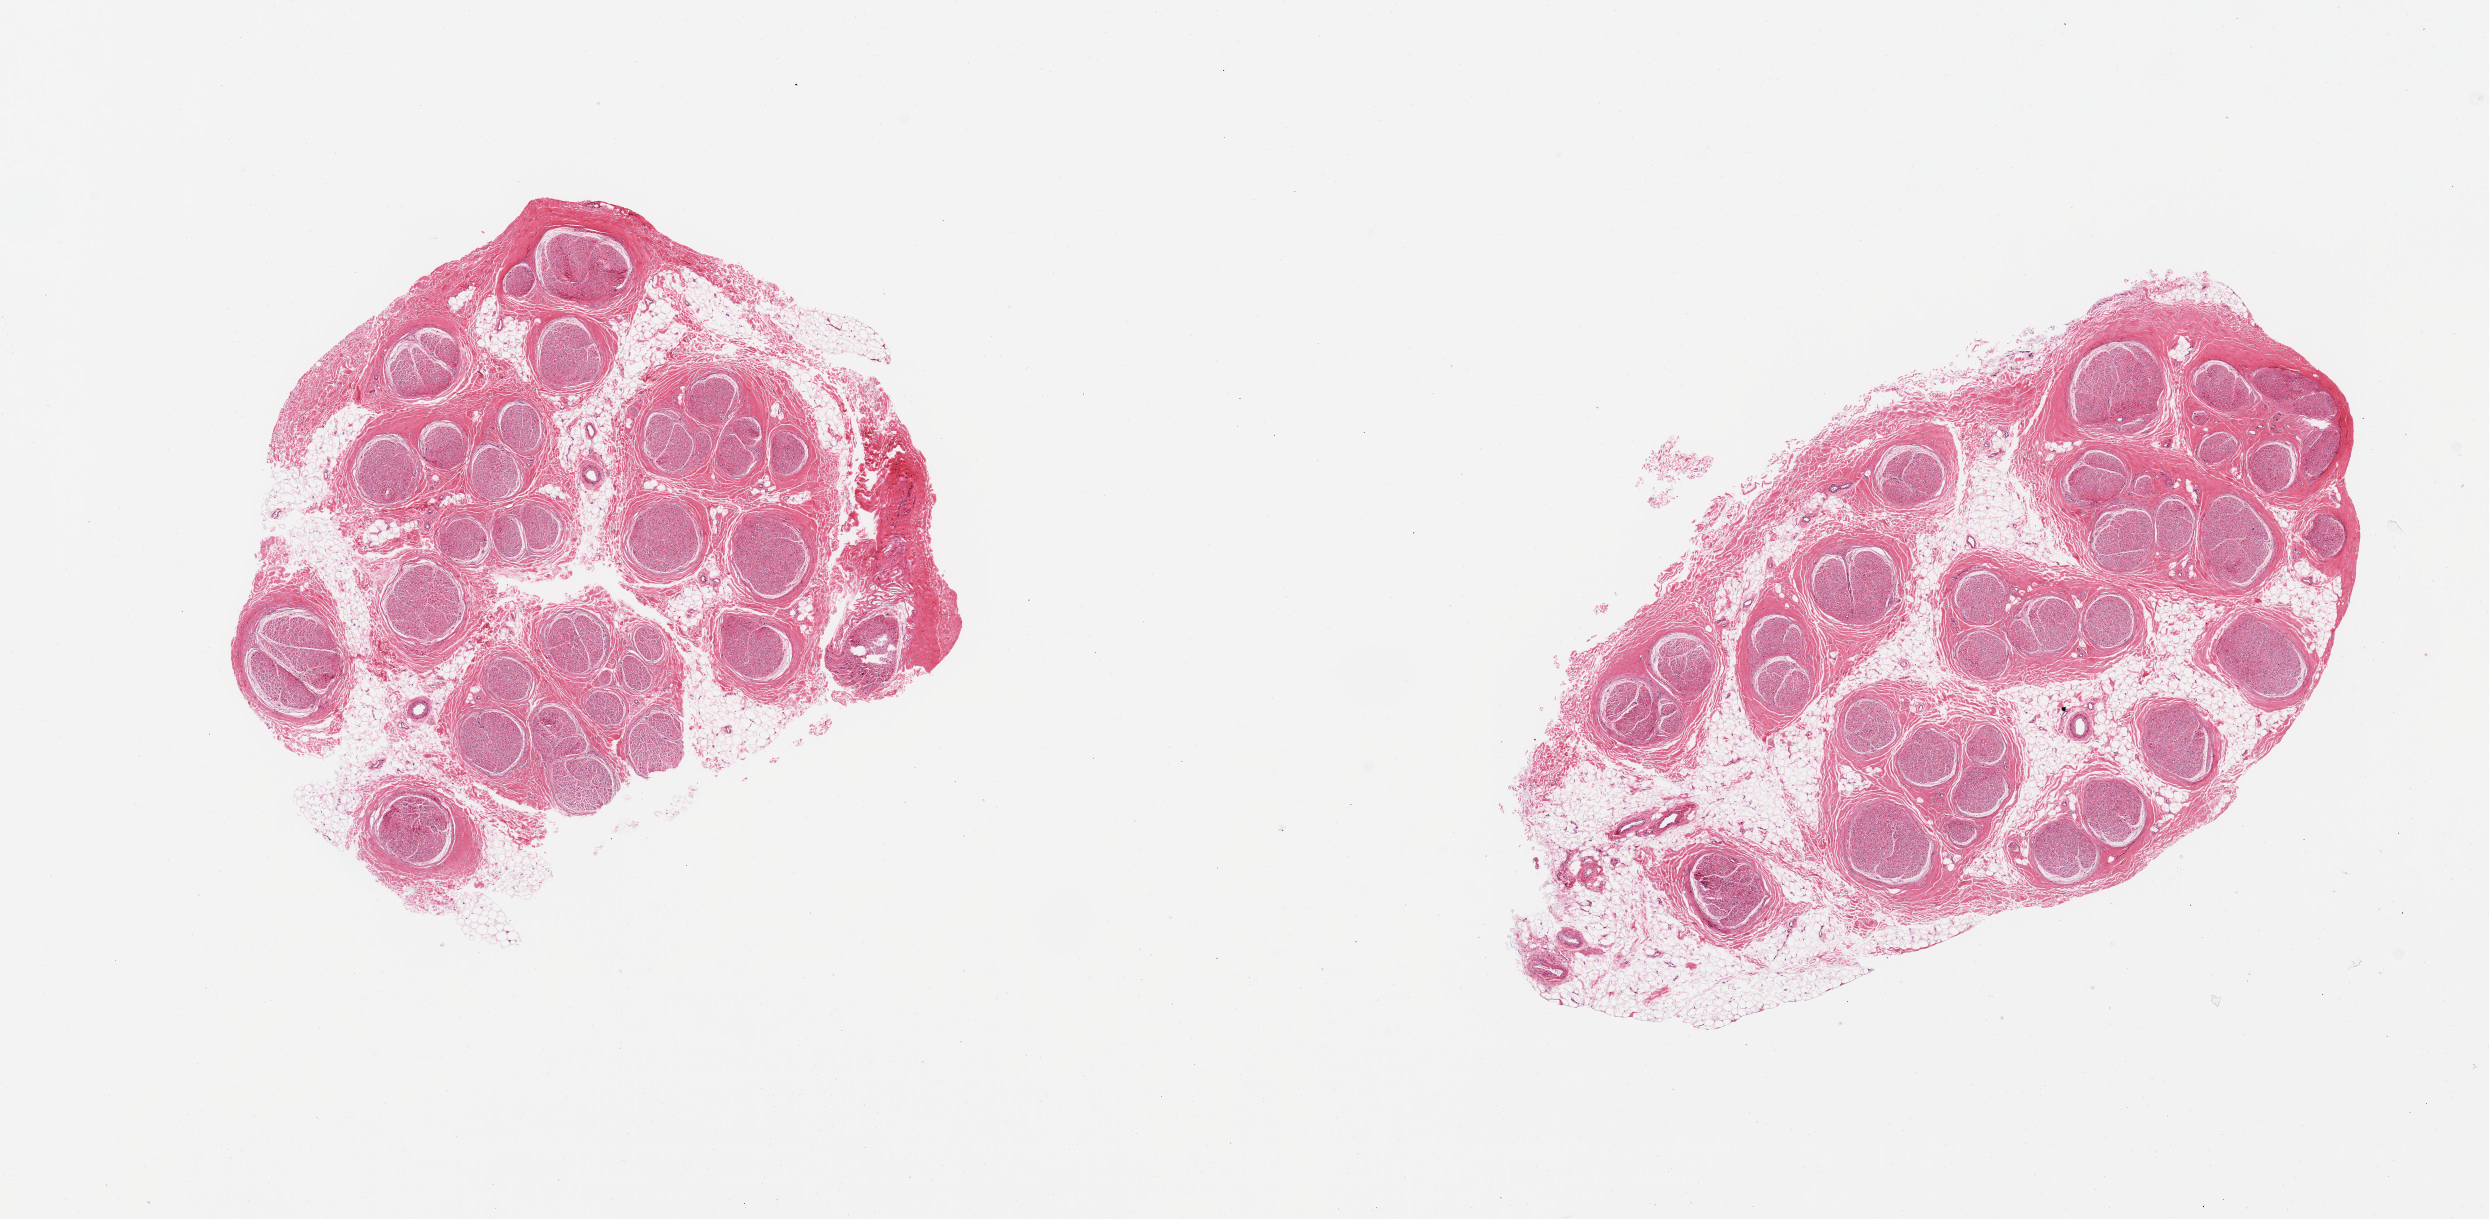
Whole-slide image, haematoxylin and eosin stain — shown as a low-resolution overview of the whole scanned area (about 19.7 x 9.6 mm, acquisition: 20x scan). PAXgene-fixed paraffin-embedded (PFPE) section. Sampled site (target tissue): tibial nerve. Donor tissue sample. Male donor.
Reviewer comment on this tissue sample: 2 pieces, trace nubbin of adherent fat, ~1mm.